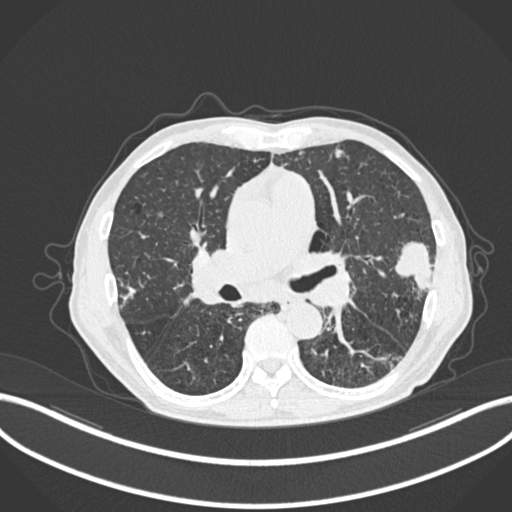
Chest CT, one axial slice; slice 131 of 287 in the series (ordered by position); reconstruction kernel B30f; lung window (W 1500 / L -600 HU); 512 × 512 image matrix, field of view 400 × 400 mm. Patient: male, 74 years. Case-level facts recorded for this patient, not image findings: clinical TNM (as recorded): T2a N1 M0.
Structures marked on this image (bounding box drawn by a radiologist):
- lung tumour (recorded histology: adenocarcinoma): box from (x=388, y=235) to (x=434, y=297) px